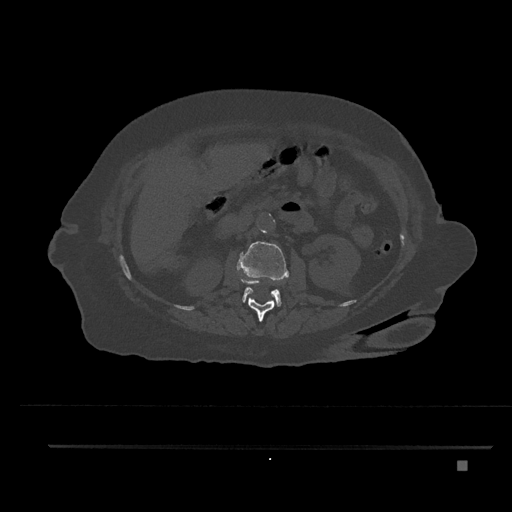
CT including the spine, one axial slice. Slice 203 of 797 in the series (ordered by position). Reconstruction kernel Br40s/3. 120 kVp. Bone window (W 1800 / L 400 HU). 0.5 mm slice thickness. 512 × 512 image matrix, field of view 437 × 437 mm. Female patient, age 76 years. Case-level facts recorded for this patient, not image findings: primary cancer: lung; vertebrae with lytic lesions (as recorded): T11, L3.
Structures marked on this image (semi-automatically segmented with operator editing):
- L1 vertebra: bounding box (x1, y1, x2, y2) in pixels: (240, 277, 276, 322)
- L2 vertebra: (237, 241, 289, 306)